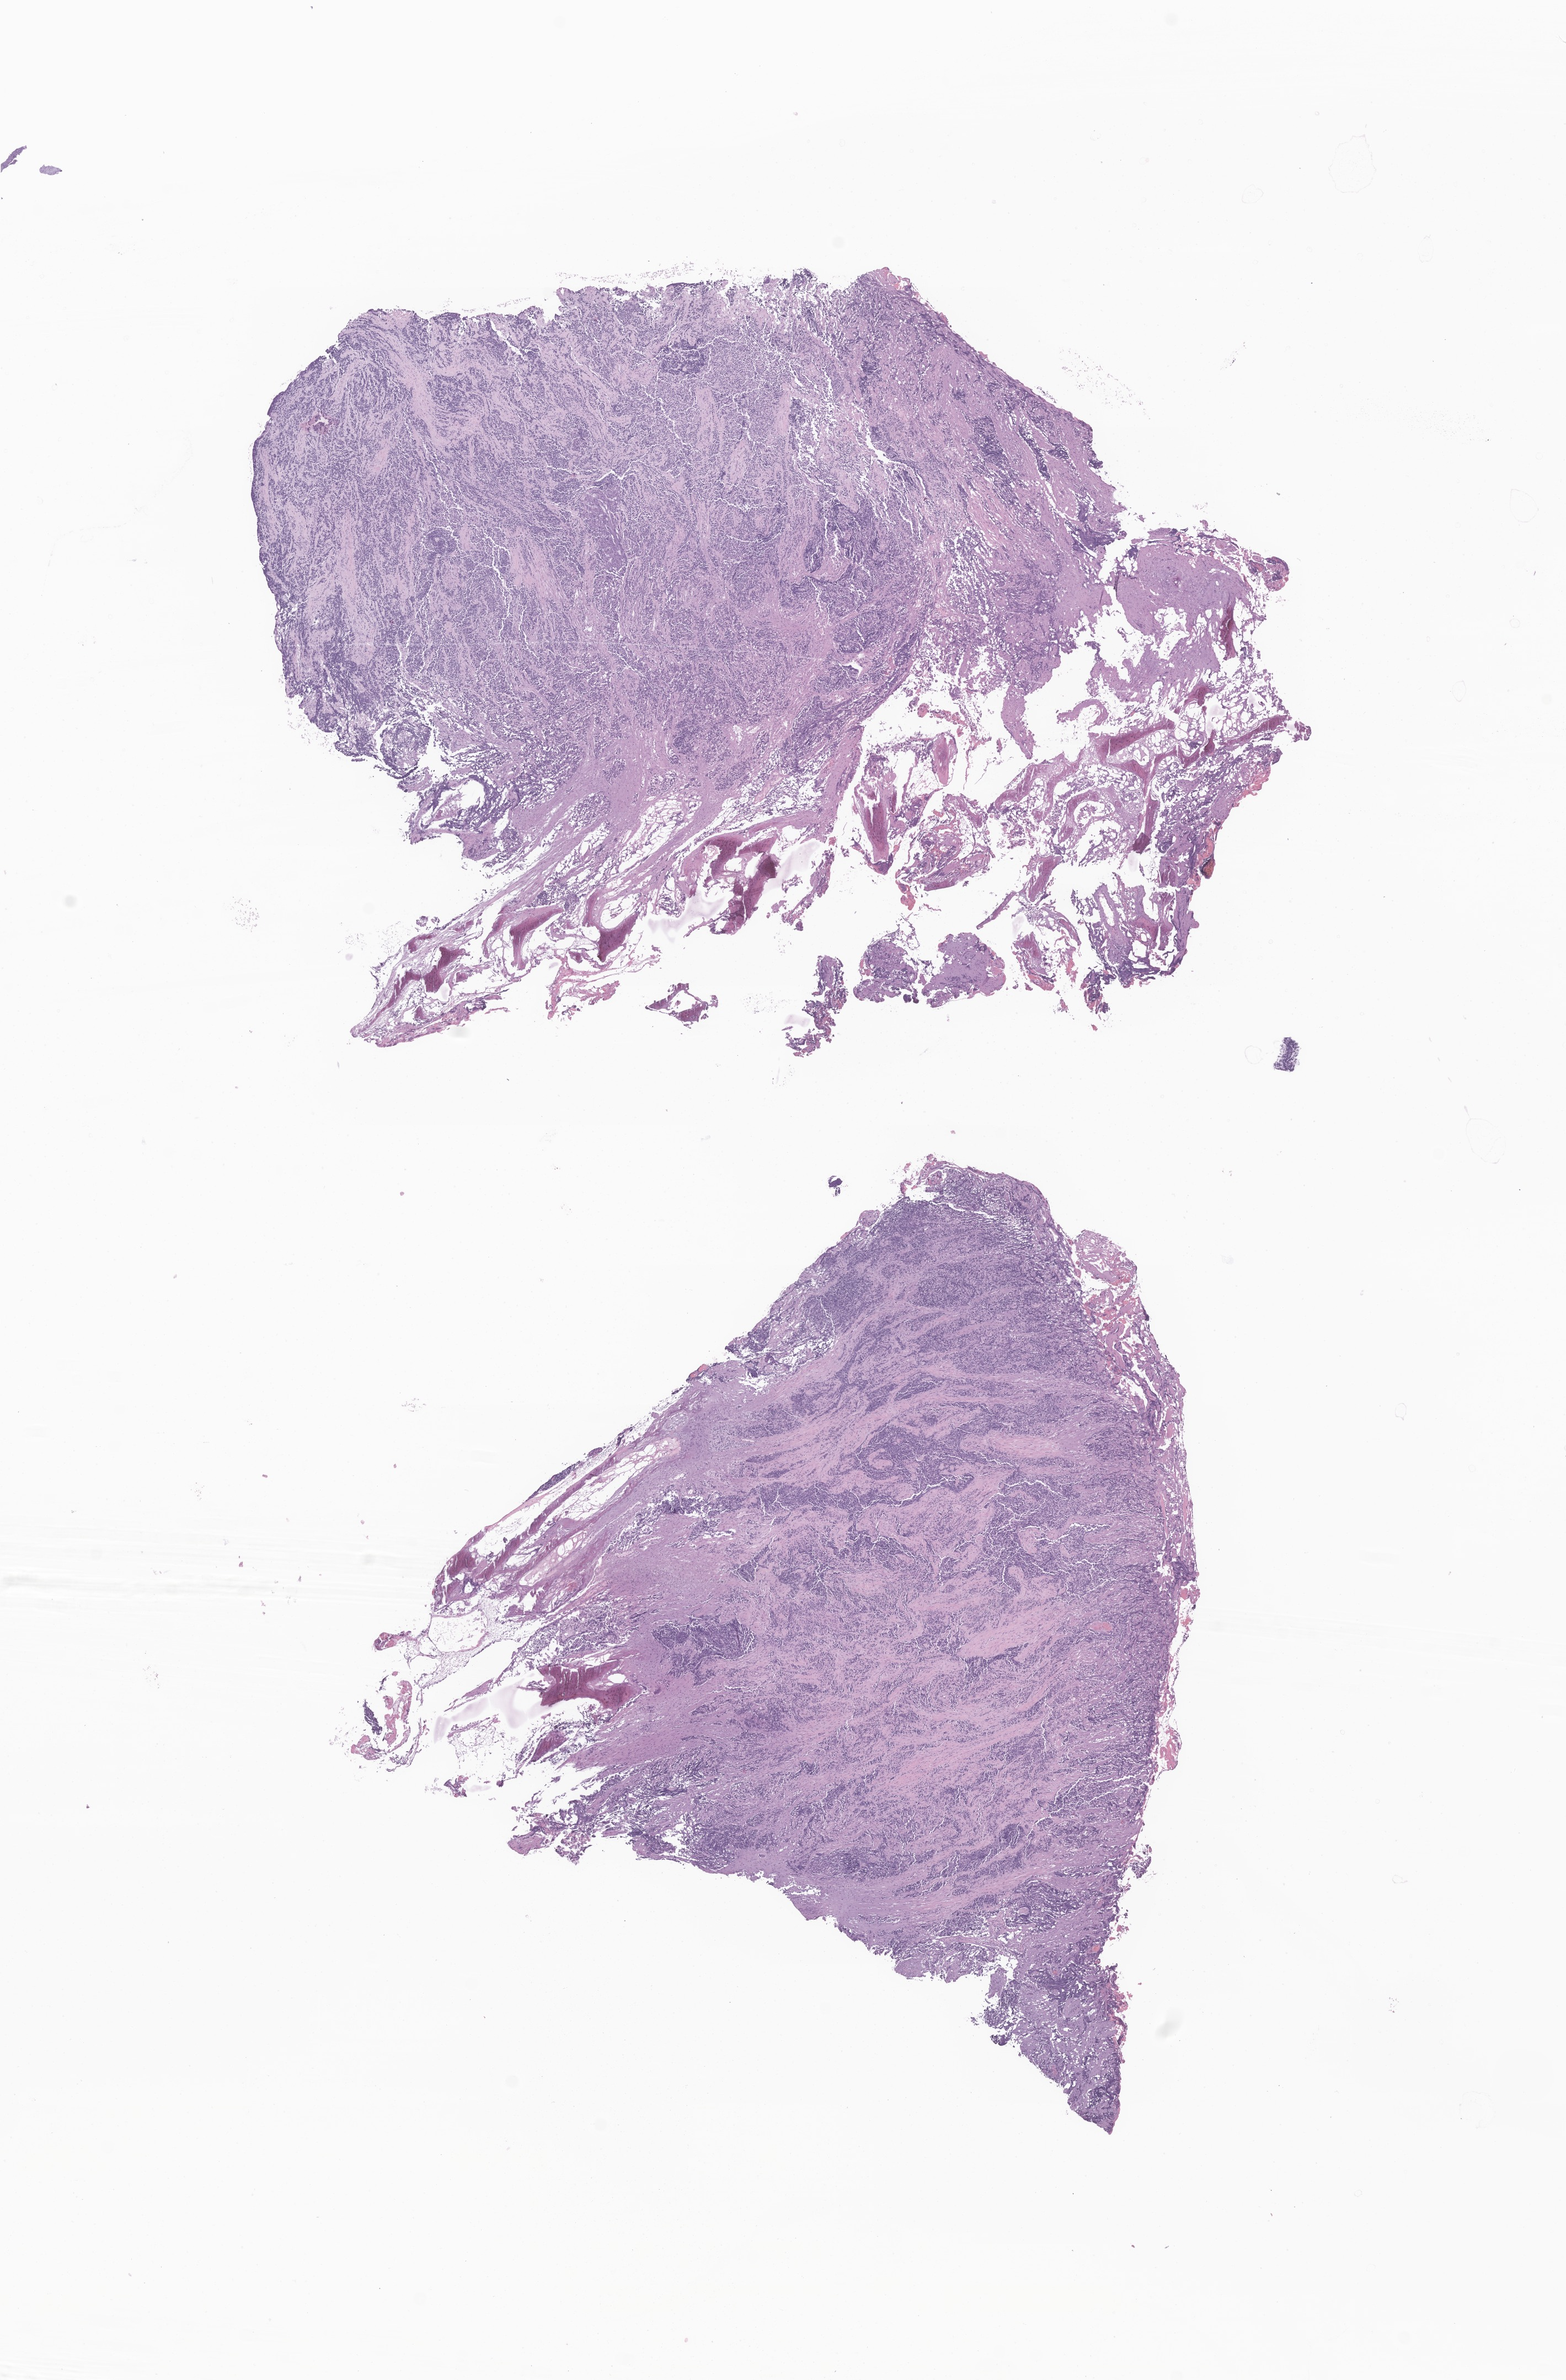
Whole-slide image, haematoxylin and eosin stain of tumor tissue from the head and neck — whole scanned area (about 12.0 x 18.2 mm) shown as a low-resolution overview; formalin-fixed paraffin-embedded section. Patient: male, age 61 months (5 years 1 month).
• diagnosis (ICD-O-3 morphology term): Neuroblastoma, NOS